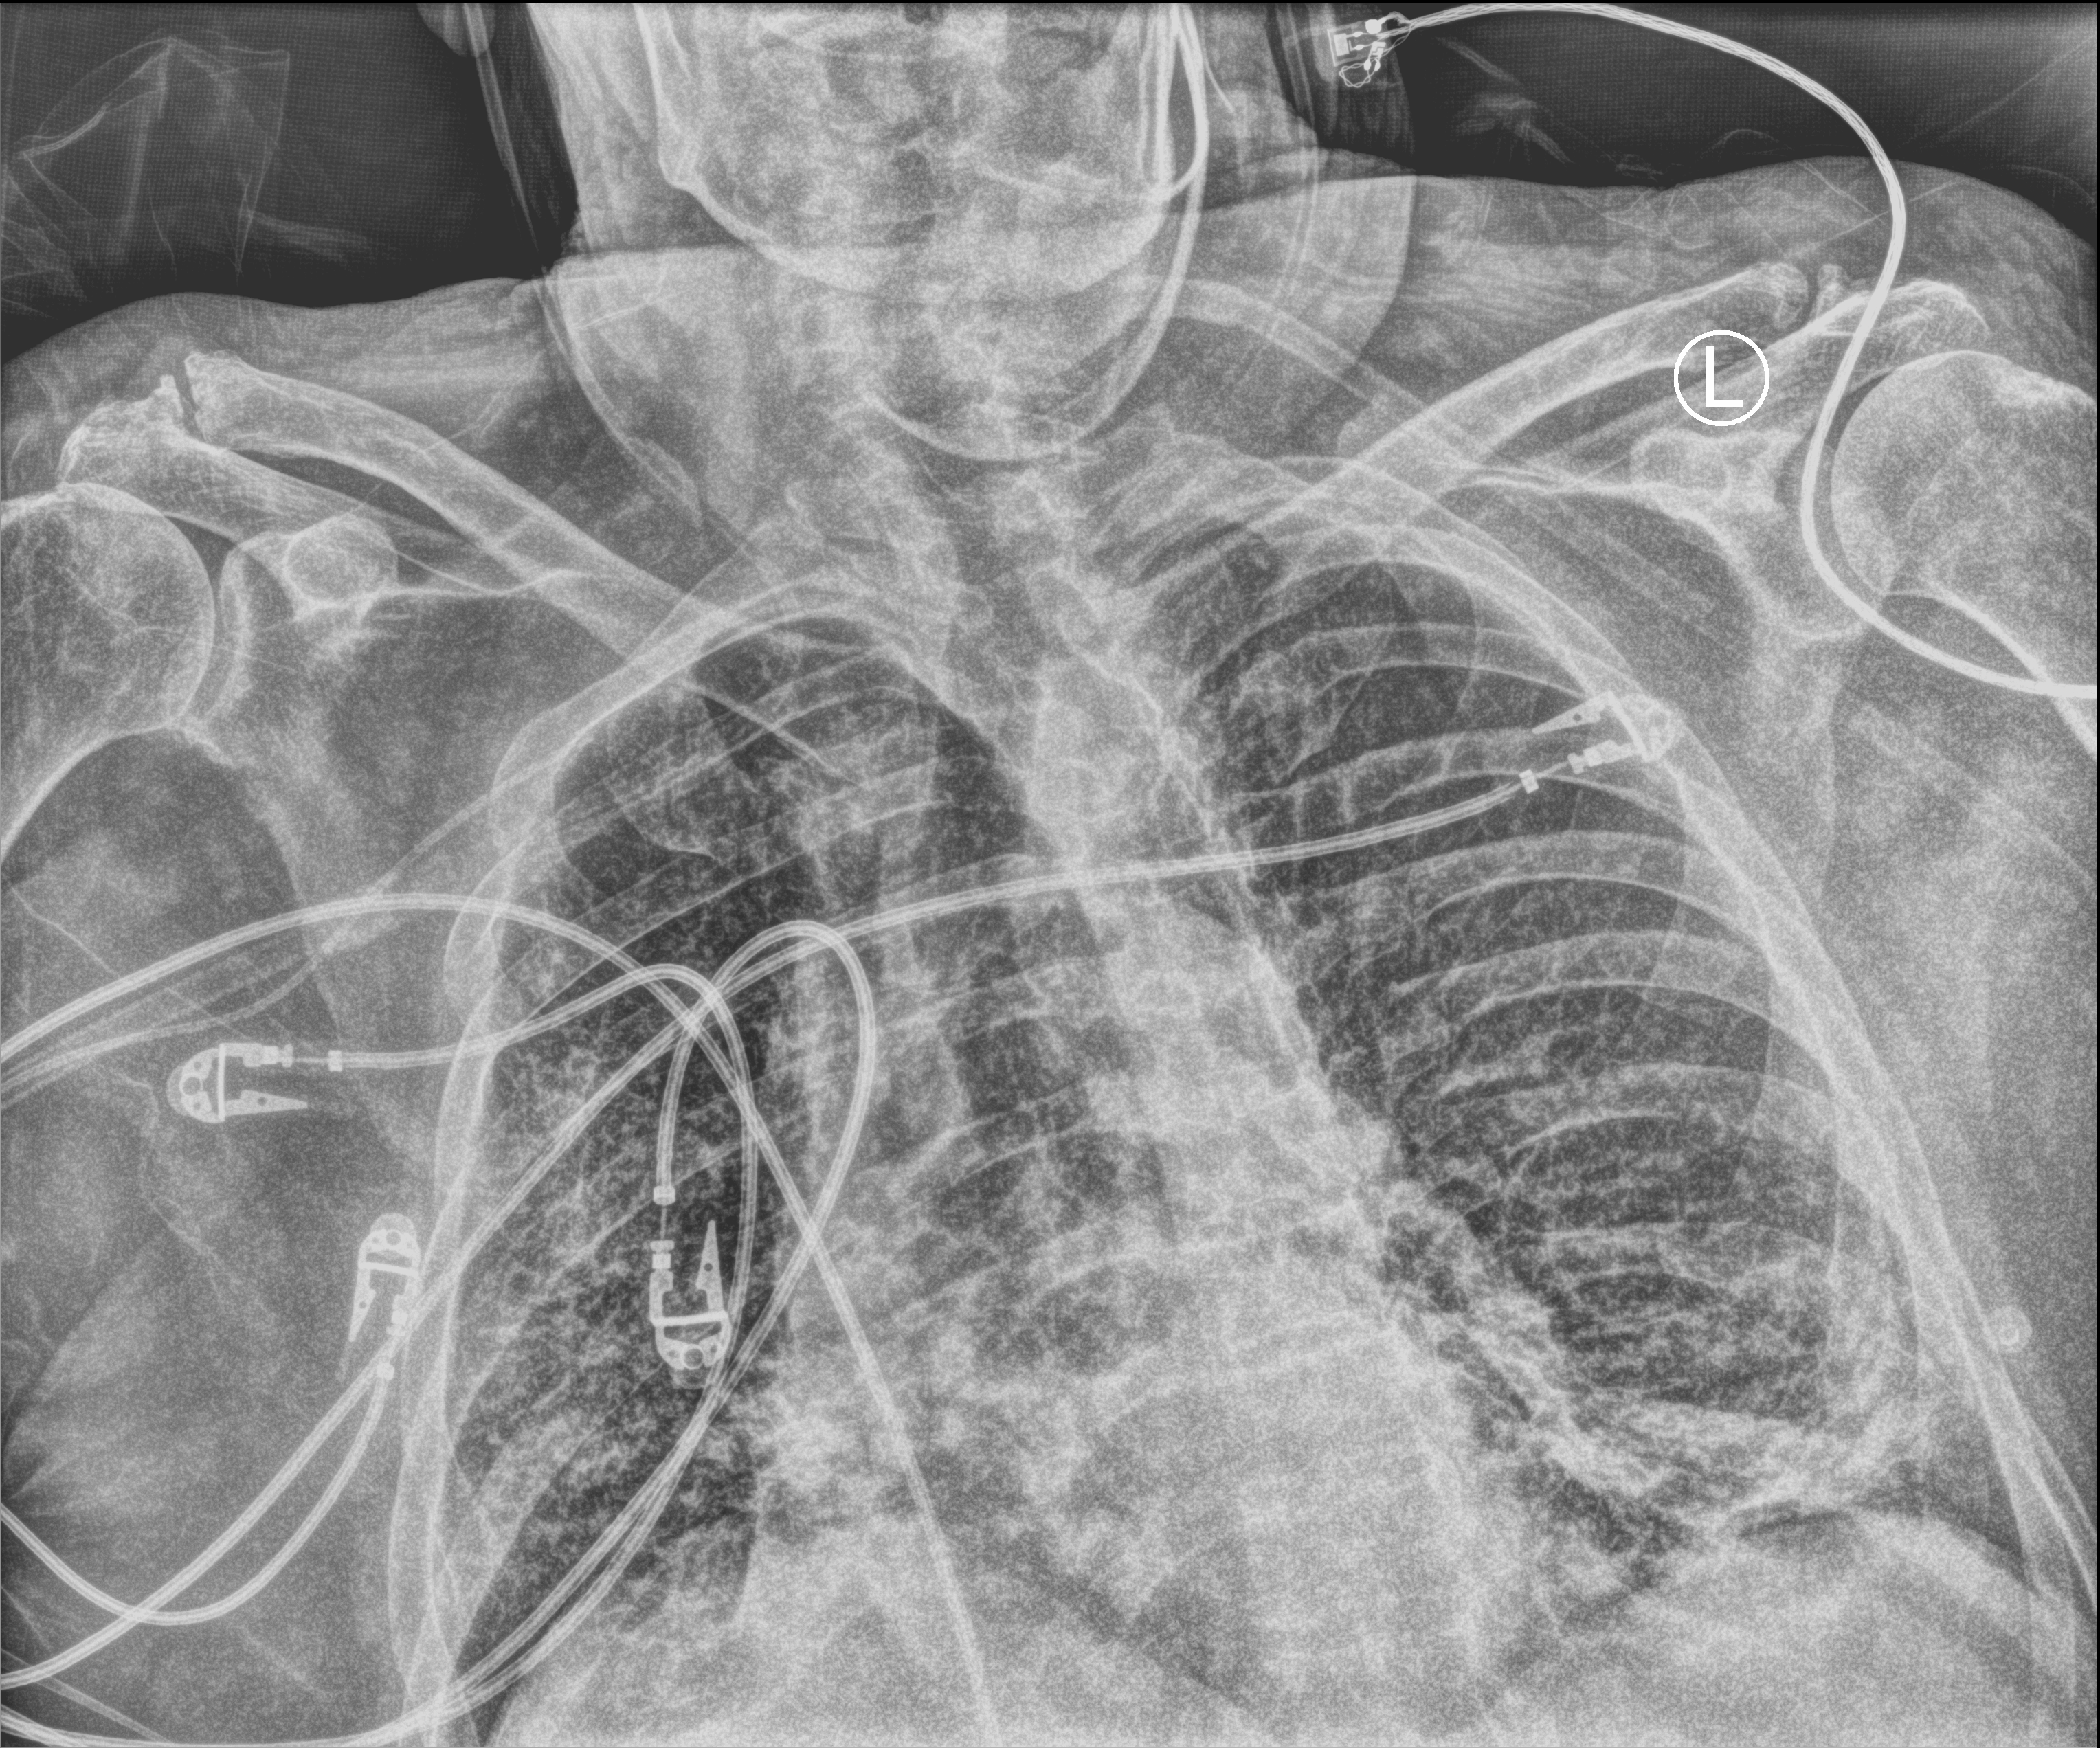
Bedside chest radiograph (computed radiography), anteroposterior (AP) projection. Patient hospitalised with COVID-19; male, aged 60–74 years.
From the hospital-stay record, not from the radiograph (when in the stay this image was taken is not recorded):
- admitted to intensive care during this hospital stay: no
- other chronic lung disease (admission record): no
- length of hospital stay: 30 days